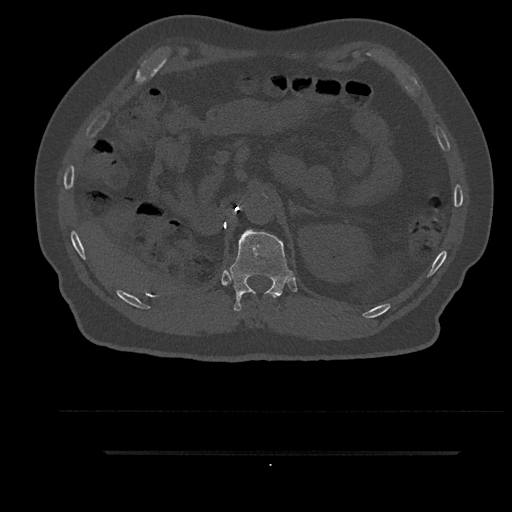
CT including the spine, one axial slice; reconstruction kernel Br40s/3; bone window (W 1800 / L 400 HU); 512 × 512 image matrix, field of view 432 × 432 mm. Patient: male, 63 years. From the clinical record (not read from this slice): primary cancer: renal; vertebrae with lytic lesions (as recorded): T8.
Structures marked on this image (semi-automatically segmented with operator editing):
- T11 vertebra: bounding box (x1, y1, x2, y2) in pixels: (273, 296, 276, 298)
- T12 vertebra: (227, 229, 293, 311)